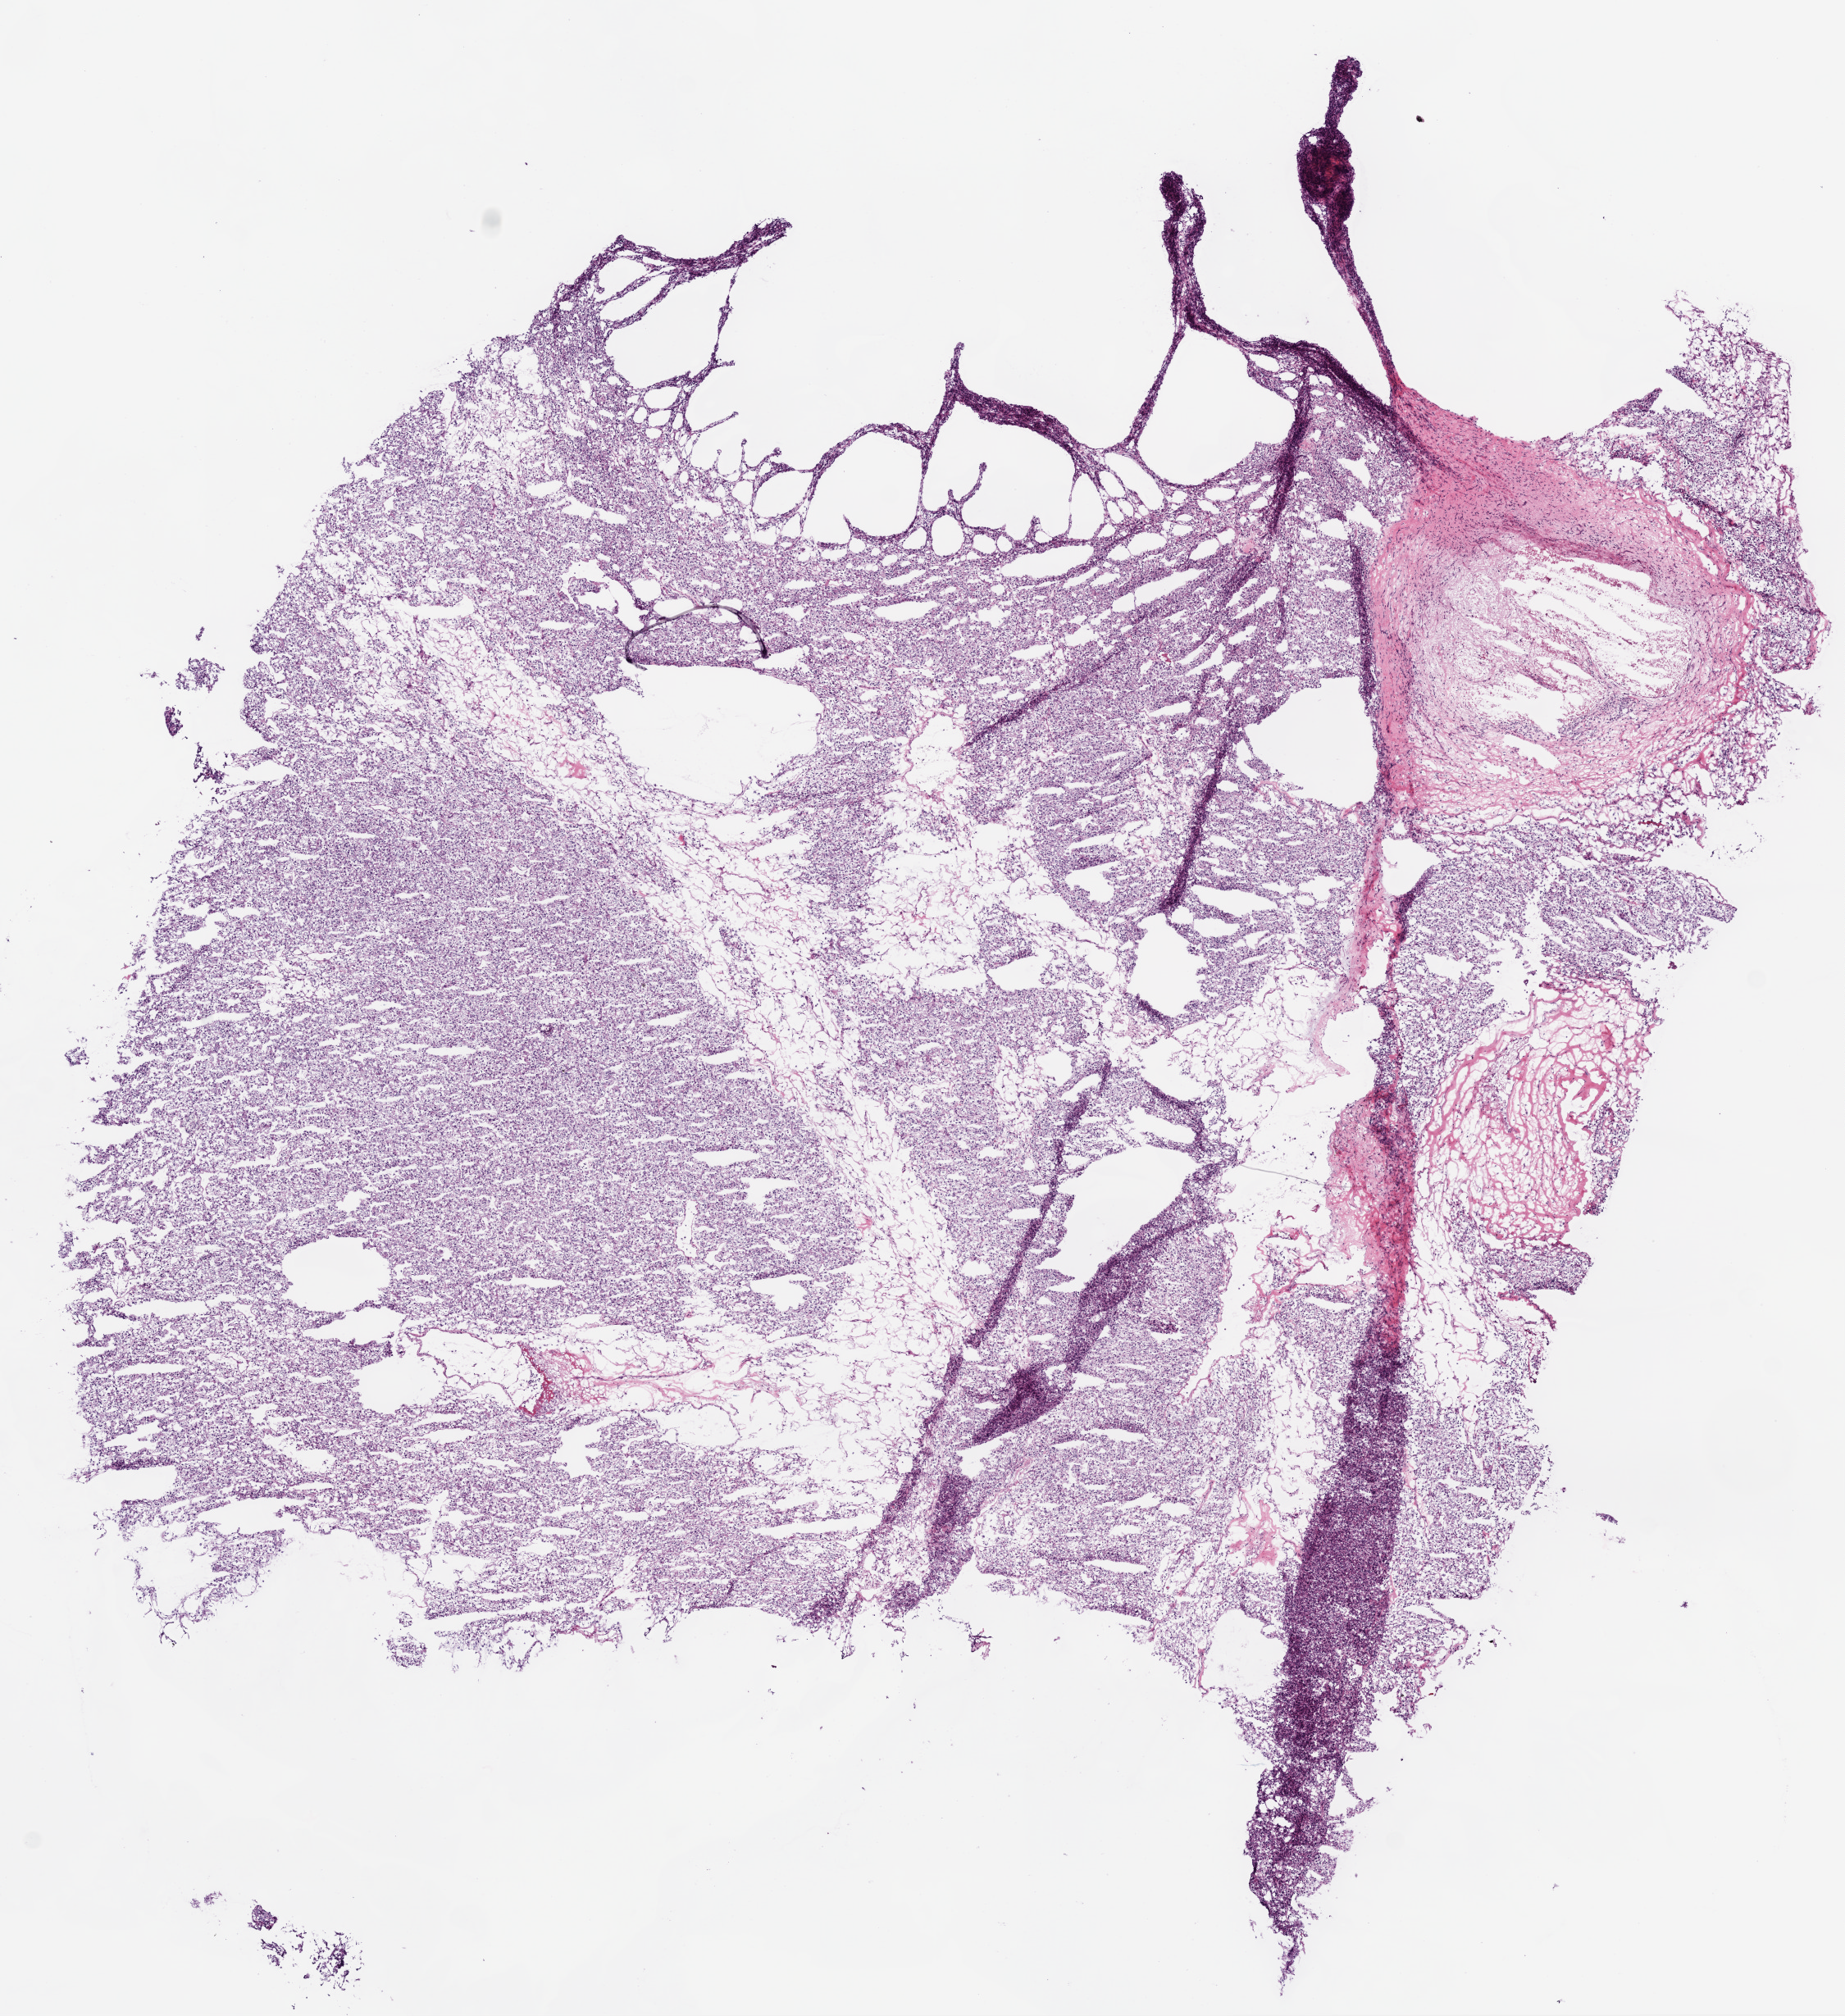
Whole-slide histology image, Hematoxylin and eosin (H&E) stained, whole scanned area (about 9.0 x 9.9 mm, acquisition: 20x scan) shown as a low-resolution overview, frozen section, kidney, primary tumour sample. Male patient; age at initial diagnosis 64 years. Histologic grade: G2 (moderately differentiated). Composition of this section per pathologist review: tumour cells 85%, tumour nuclei 80%, normal cells 0%, stromal cells 15%, necrosis 0%.
AJCC pathologic stage: III. TNM: T3 NX M0. Pathologic diagnosis: Clear cell adenocarcinoma, NOS.